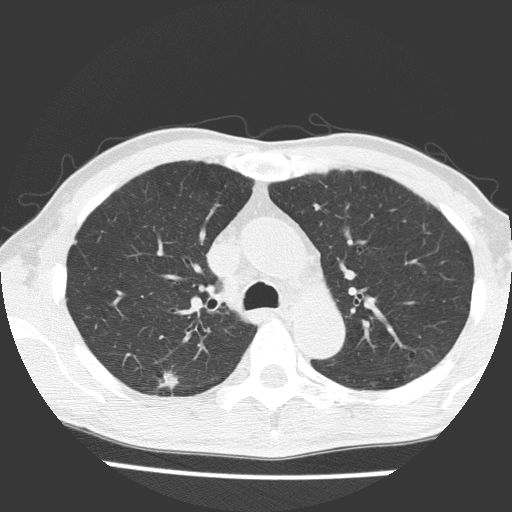
Axial slice from a low-dose chest CT screening exam; first (baseline) screen; lung window (W 1500 / L -600 HU); 2 mm slice thickness; lung (sharp) reconstruction kernel (FC51); 120 kVp. Male participant, aged 66 years at enrolment. Current smoker at enrolment.
Expert reader's lesion annotation, bounding box (x1, y1, x2, y2) in pixels: (136, 356, 195, 410). The exam's reader record, not a measurement of the box and not confirmed to be the same lesion: non-calcified nodule or mass ≥4 mm, right upper lobe, 15 × 10 mm, spiculated (stellate) margins, soft tissue attenuation. Official screen result: positive, change unspecified: nodule(s) >= 4 mm or enlarging nodule(s), mass(es), or other non-specific abnormalities suspicious for lung cancer. Participant outcome: lung cancer diagnosed 43 days after this screen — adenocarcinoma, NOS, right upper lobe, moderately differentiated (G2), stage IB (AJCC 6th edition), 11 mm at pathology.